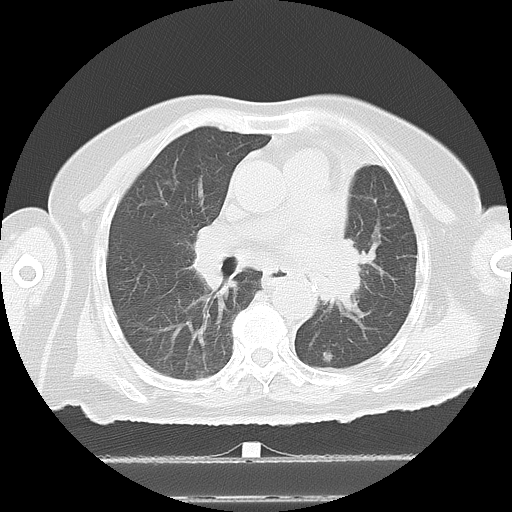
Chest CT, one axial slice. Position 8 of 27 along the scan axis. Reconstruction kernel LUNG. Lung window (W 1500 / L -600 HU). 512 × 512 image matrix, field of view 350 × 350 mm. Patient: female, 67 years. From the clinical record (not read from this slice): clinical TNM (as recorded): T1a N1 M1c.
Structures marked on this image (rectangle marked by the reading radiologist):
- lung tumour (recorded histology: adenocarcinoma): box from (x=318, y=228) to (x=372, y=314) px